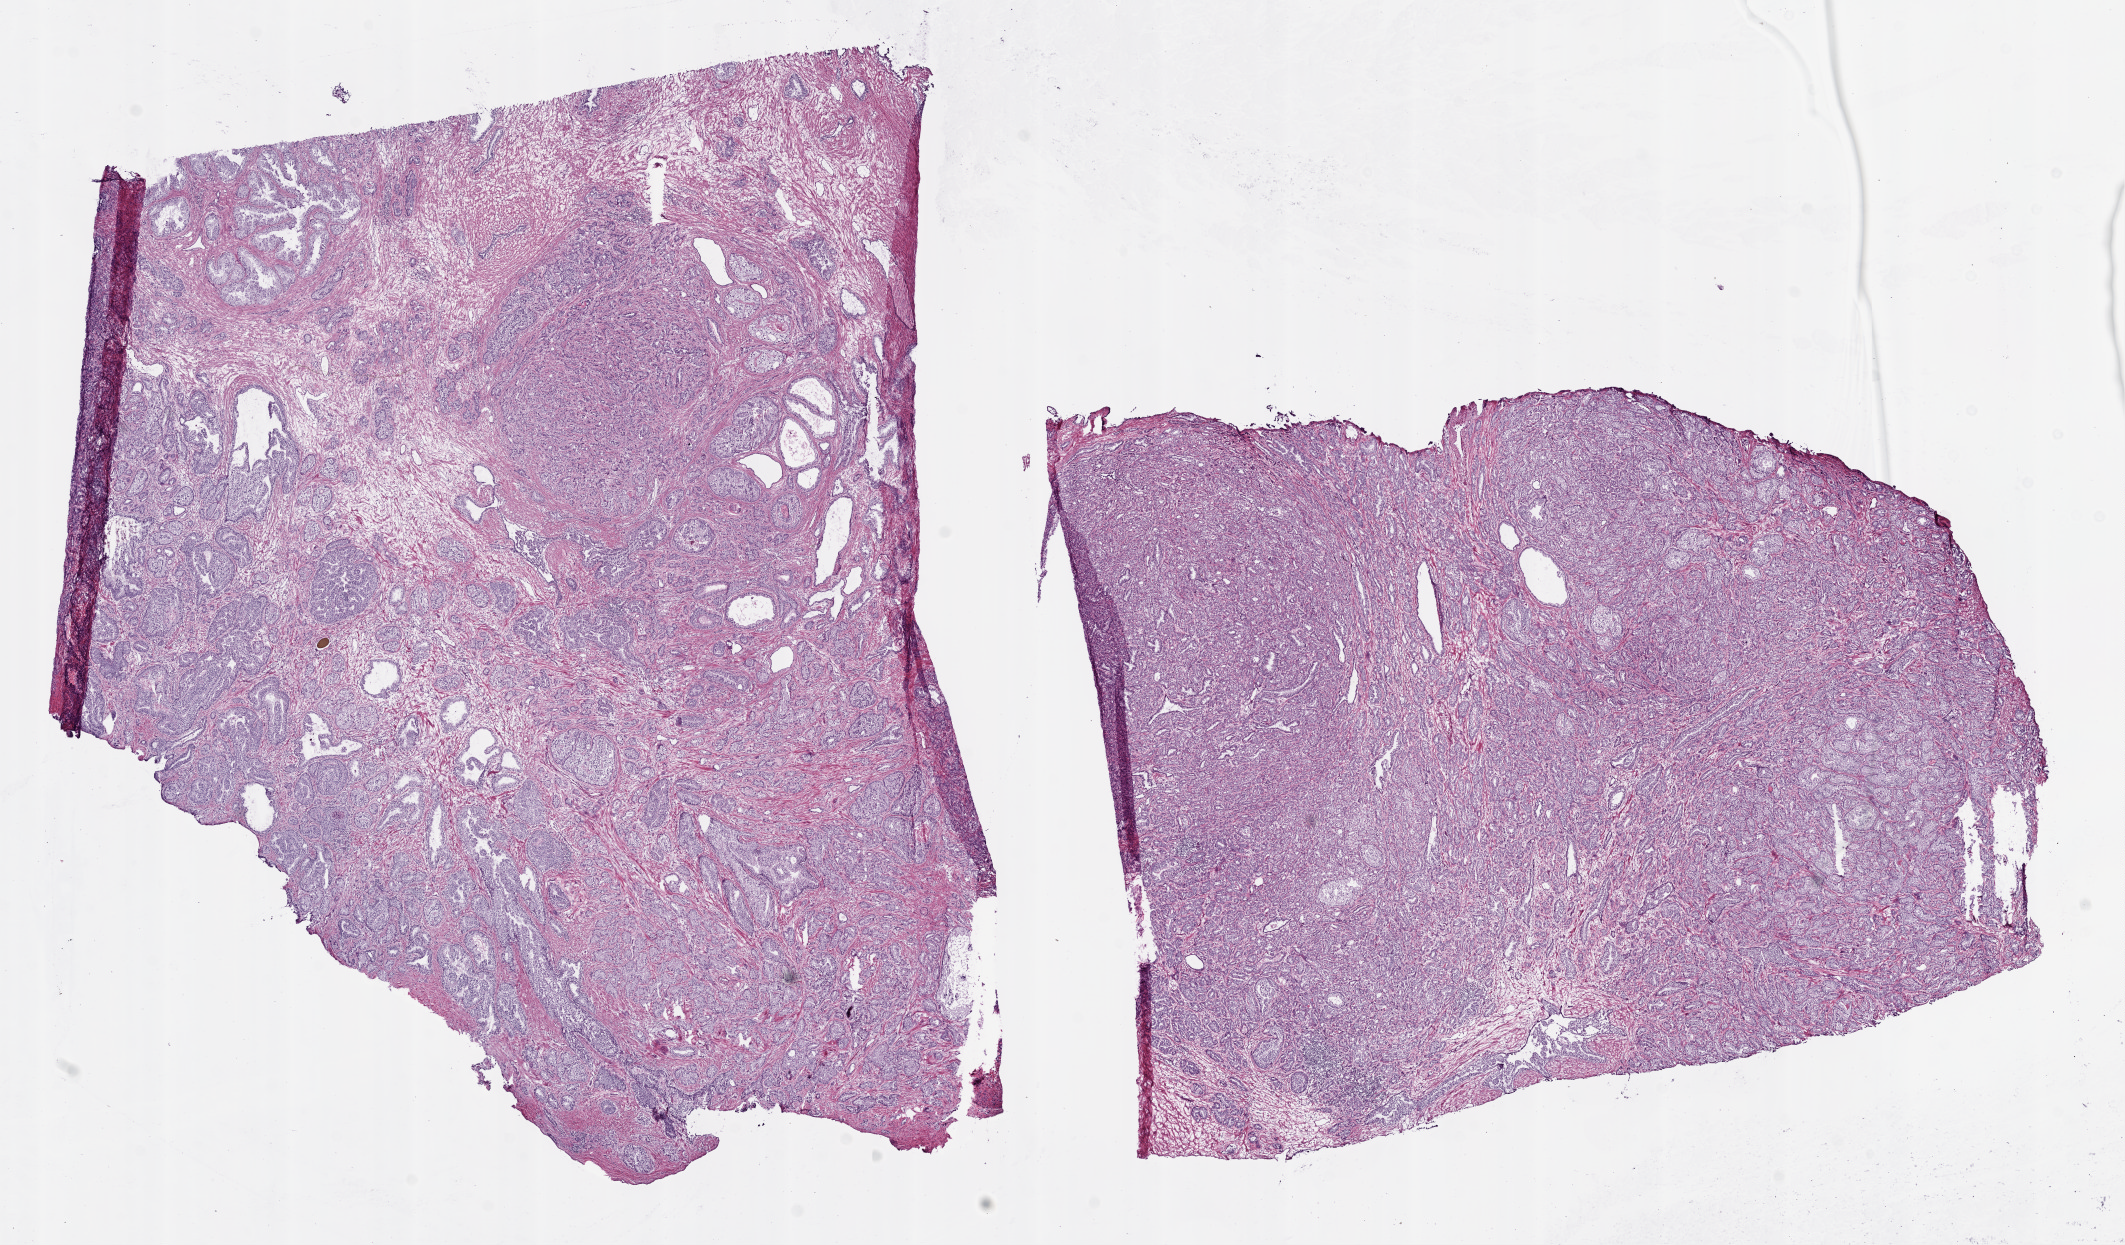
Whole-slide histology image, Hematoxylin and eosin (H&E) stained, low-resolution overview of the scanned area, about 17.1 x 10.0 mm, frozen section, primary tumour sample from the prostate. Male, age 60 years at initial diagnosis.
Pathologic diagnosis: Acinar cell carcinoma (prostate gland).